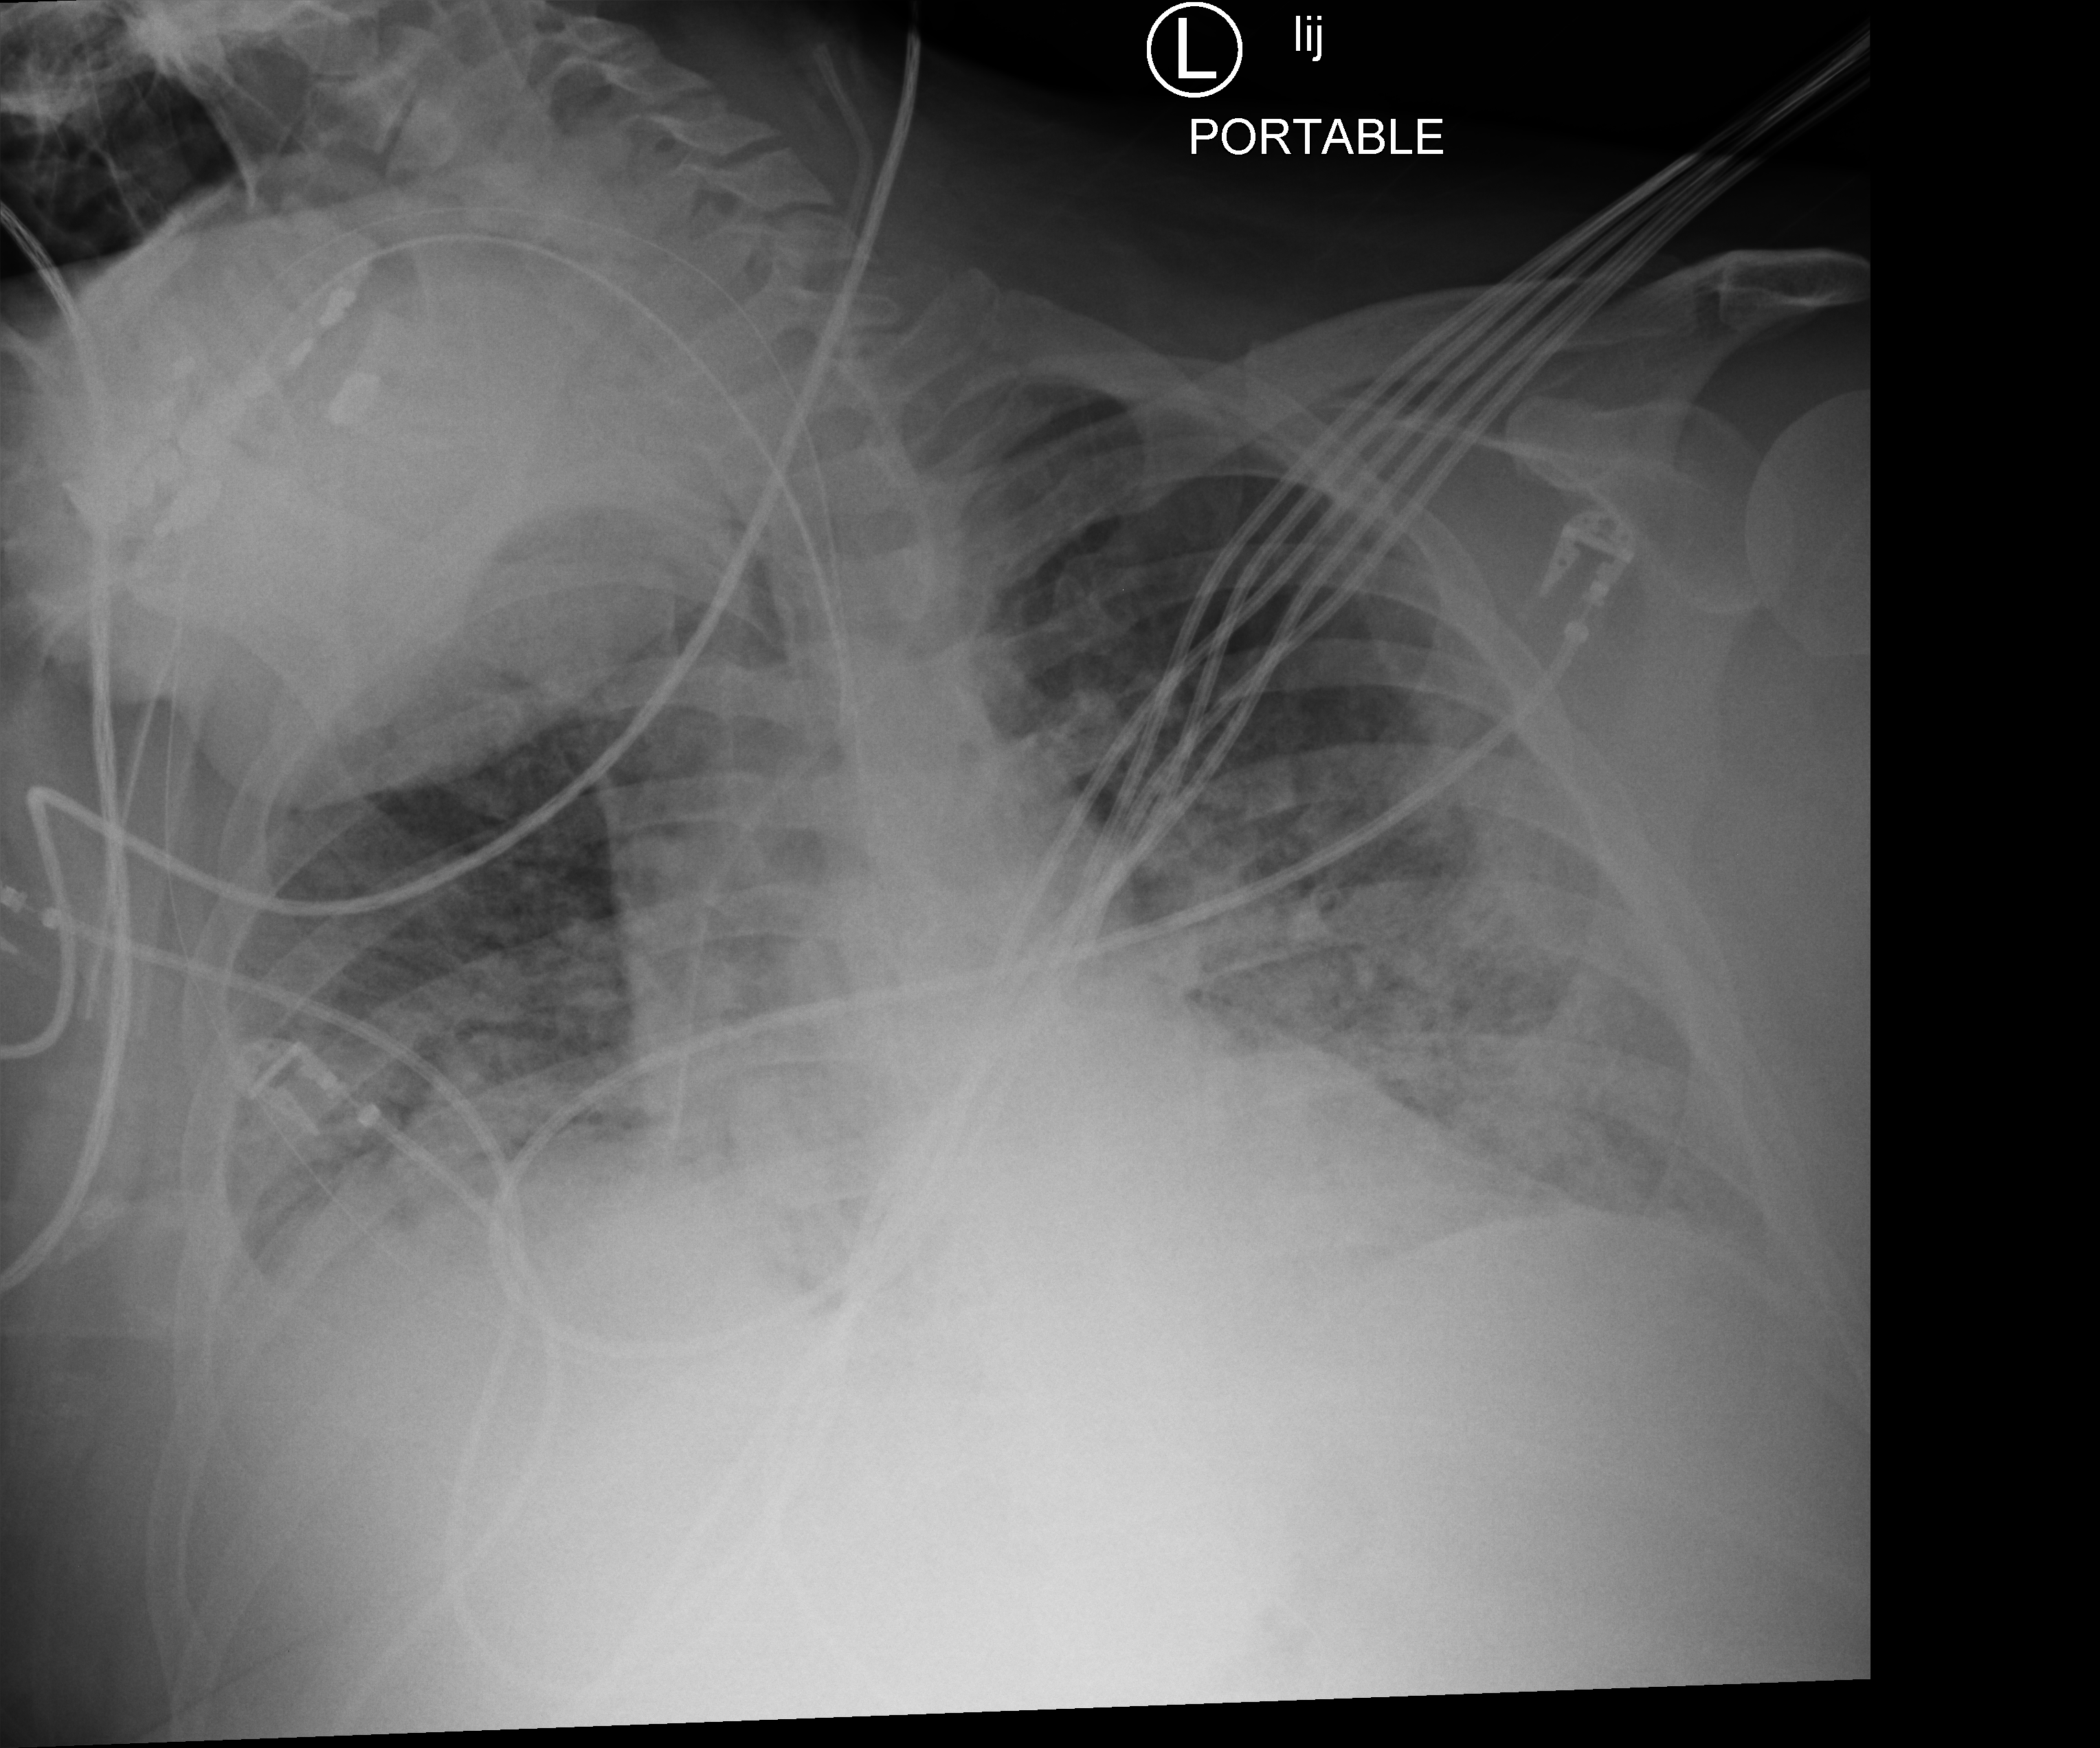
Portable chest radiograph; anteroposterior (AP) projection. Patient hospitalised with COVID-19; male, aged 18–59 years.
Hospital-stay facts (about this admission, not read from this image; timing relative to this image not recorded): admitted to intensive care during this hospital stay: yes; mechanically ventilated during this hospital stay: yes.